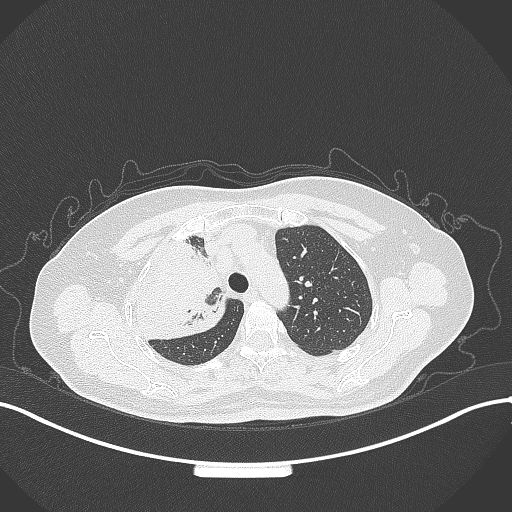
Chest CT, one axial slice. Position 242 of 309 along the scan axis. Reconstruction kernel B70f. 120 kVp. Lung window (W 1500 / L -600 HU). 1 mm slice thickness. 512 × 512 image matrix. Female patient, age 60 years. Case-level facts recorded for this patient, not image findings: clinical TNM (as recorded): T3 N1 M1.
Outlined on this slice (rectangle marked by the reading radiologist):
- lung tumour (recorded histology: adenocarcinoma): bounding box <126,233,231,344> (left, top, right, bottom; pixels)